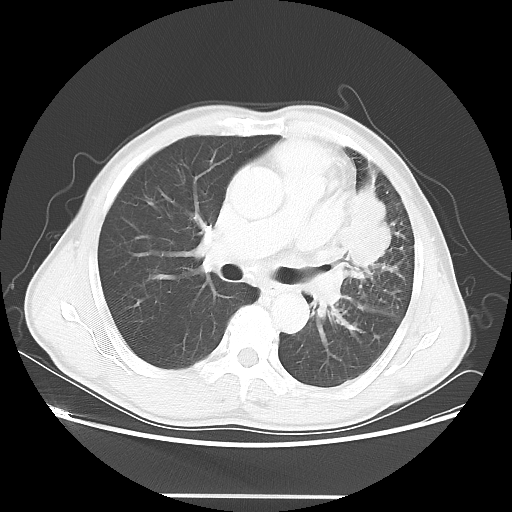
Chest CT, one axial slice. Position 30 of 55 along the scan axis. Reconstruction kernel LUNG. 100 kVp. Lung window (W 1500 / L -600 HU). 512 × 512 image matrix, field of view 398 × 398 mm. Male patient, age 60 years. From the clinical record (not read from this slice): clinical TNM (as recorded): T3 N3 M0.
Structures marked on this image (bounding box drawn by a radiologist):
- lung tumour (recorded histology: adenocarcinoma): bounding box [x1, y1, x2, y2] px = [346, 181, 395, 274]